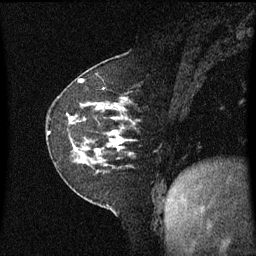
Breast MRI (dynamic contrast-enhanced), one sagittal slice. Slice 21 of 60 in the series (ordered by position). Dynamic contrast-enhanced series, image 2 of 3 at this slice position (ordered by acquisition). 1.5 T. TE 4.2 ms, TR 8.4 ms. 256 × 256 image matrix, field of view 210 × 210 mm. Patient: female, 60 years. From the clinical record (not read from this slice): setting: breast cancer imaged before/during neoadjuvant chemotherapy; receptor status: triple-negative.
Structures marked on this image (semi-automatic segmentation, software-assisted and operator-edited):
- analysis volume of interest (the breast-tissue region the enhancement analysis was run in; not a lesion): bounding box (x1, y1, x2, y2) in pixels: (48, 99, 137, 173)
- tumour enhancement mask (voxels above the 70 % enhancement threshold inside the analysis volume of interest): (49, 107, 125, 153)